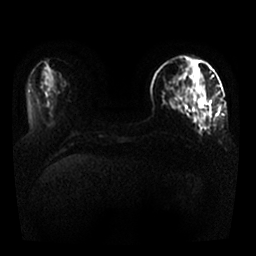
Breast MRI, one axial slice. Slice 9 of 25 in the series (ordered by position). Diffusion-weighted series; image 2 of 4 stored at this slice position (different b-values; order by instance number). 1.5 T. 256 × 256 image matrix, field of view 330 × 330 mm. Female patient.
Annotated regions visible in this slice (manually delineated by an expert):
- tumour on diffusion-weighted imaging: bounding box <199,99,207,107> (left, top, right, bottom; pixels)